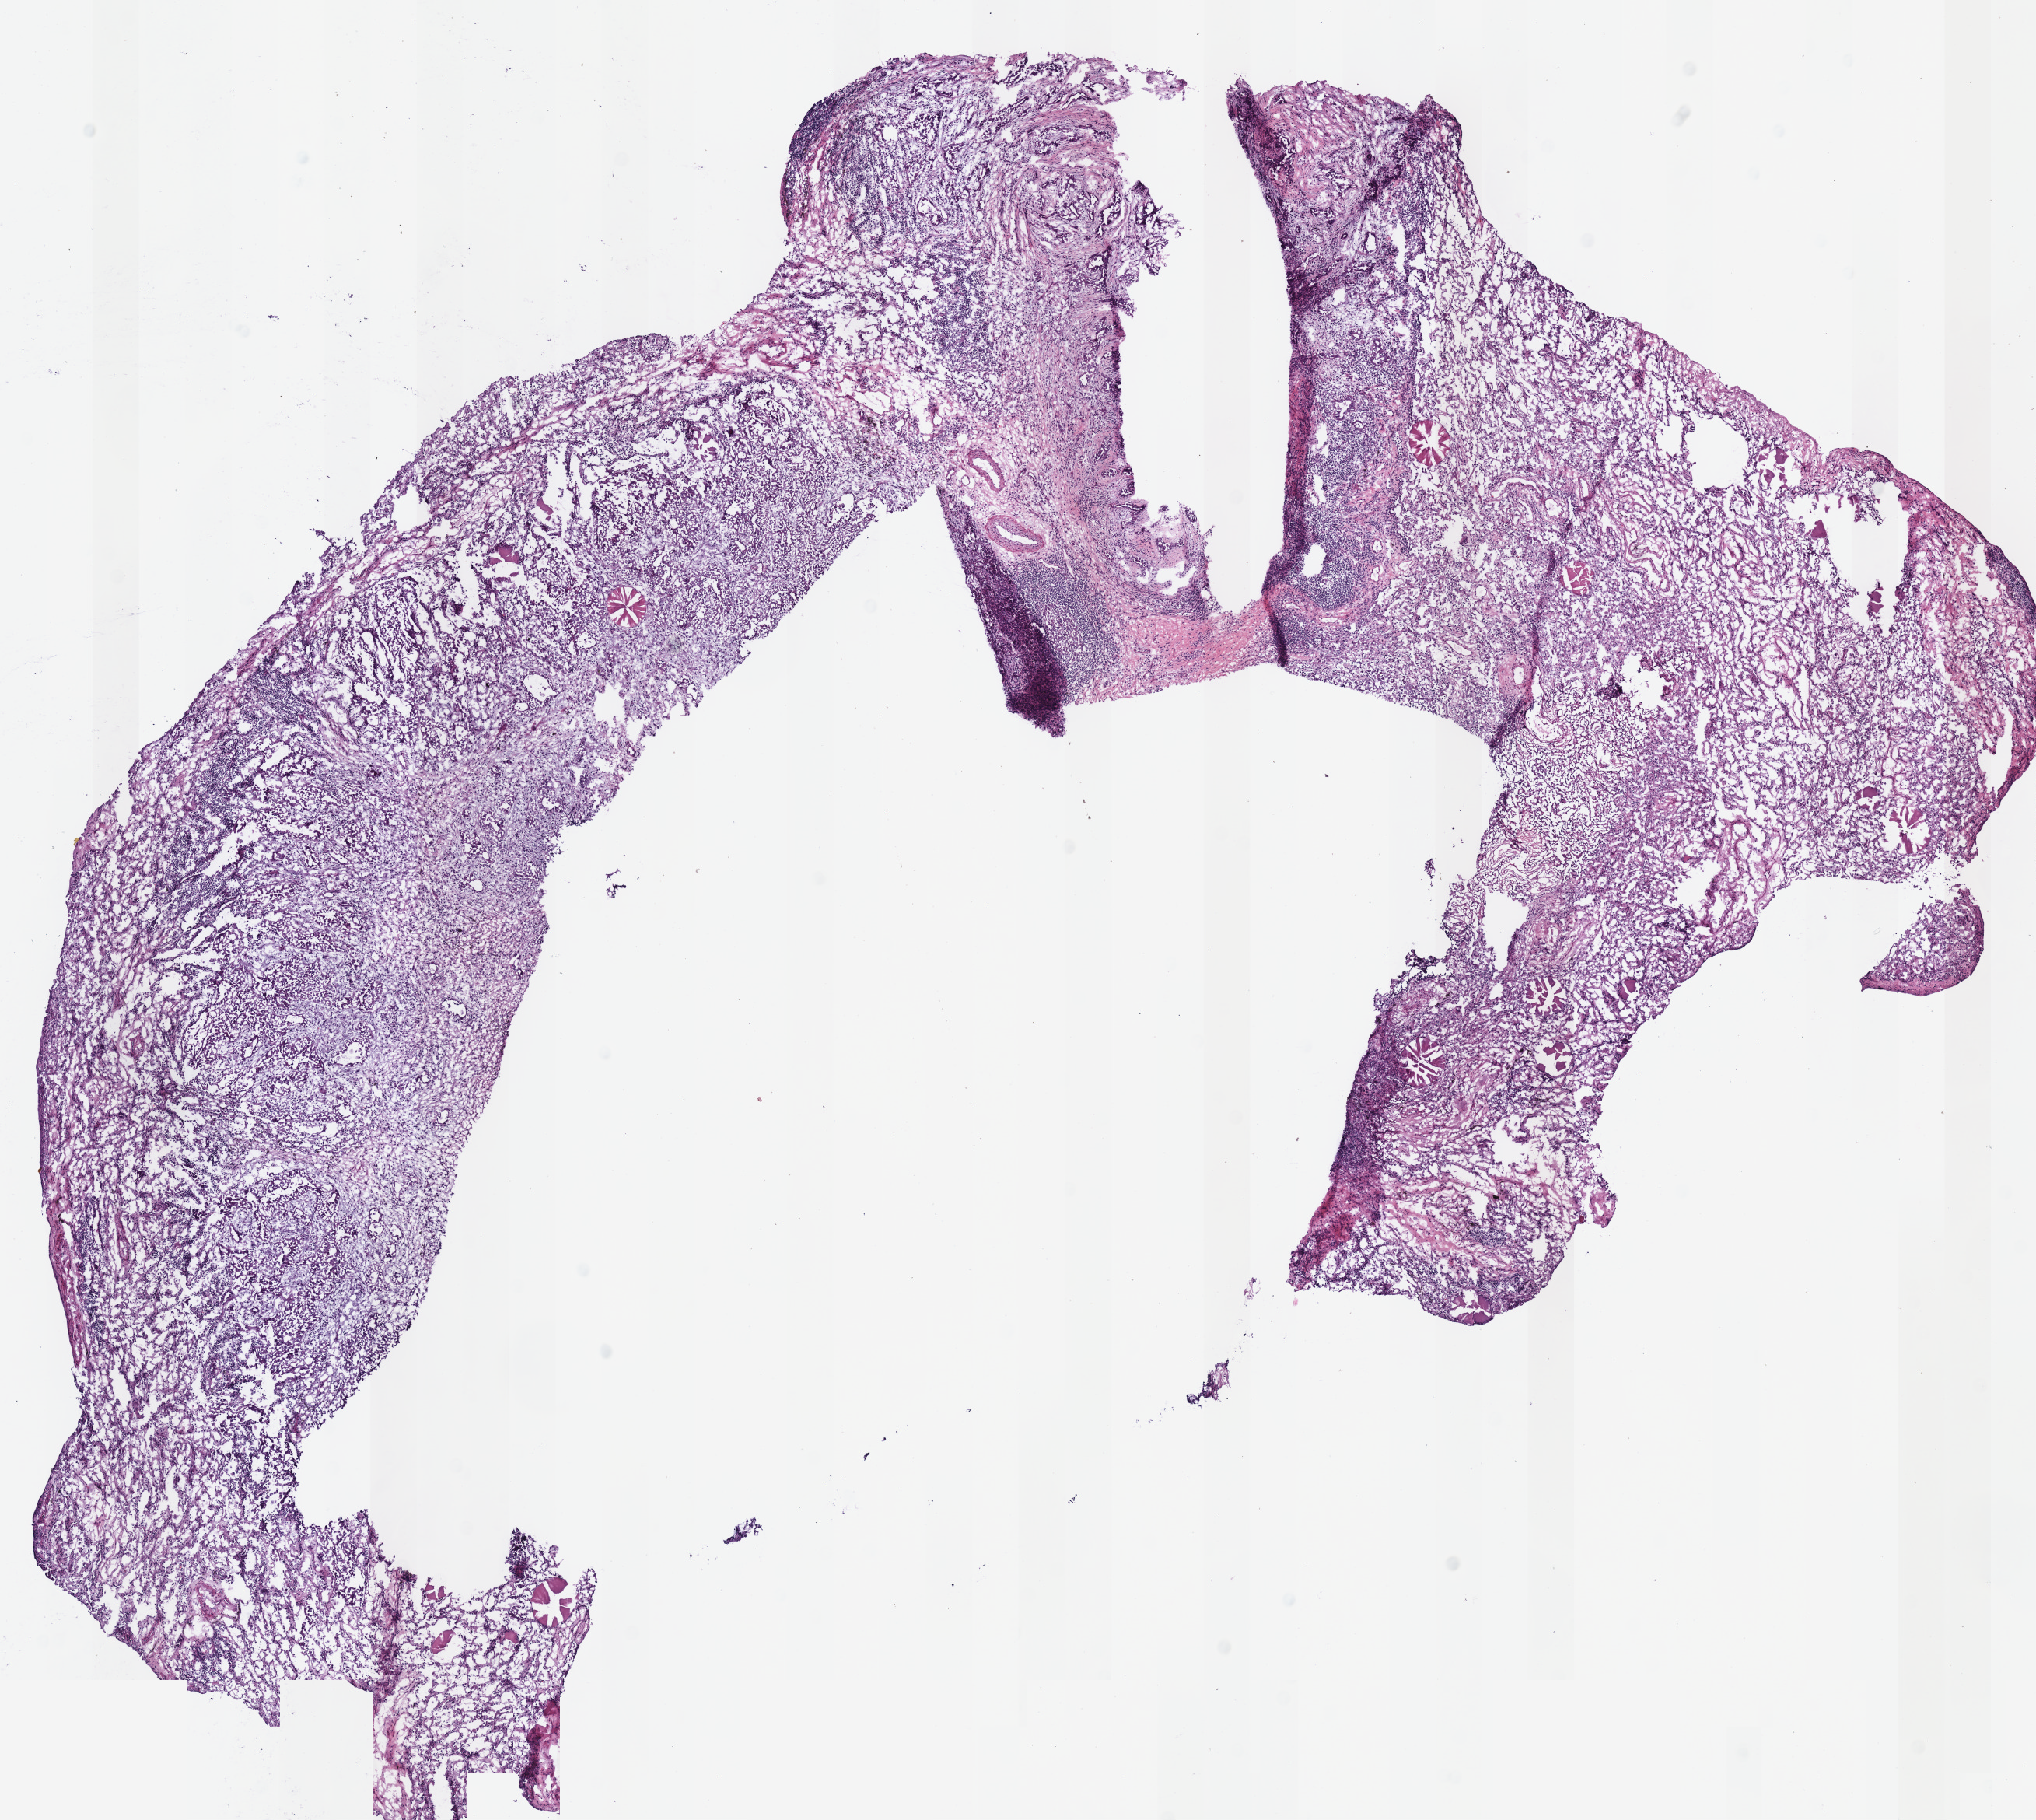
Hematoxylin and eosin (H&E) stained whole-slide image, shown as a low-resolution overview of the whole scanned area (about 10.3 x 9.2 mm), frozen section from the bottom of the tissue portion, sample: primary tumour, lung. Female patient; age at initial diagnosis 72 years. Composition of this section per pathologist review: tumour cells 70%, tumour nuclei 55%, normal cells 30%, stromal cells 0%, necrosis 0%. Inflammatory infiltration, as recorded: lymphocyte infiltration 20%, monocyte infiltration 10%, neutrophil infiltration 0%.
* AJCC pathologic stage: IIB
* histologic diagnosis: Papillary adenocarcinoma, NOS (upper lobe, lung)
* TNM: T2b N1 M0